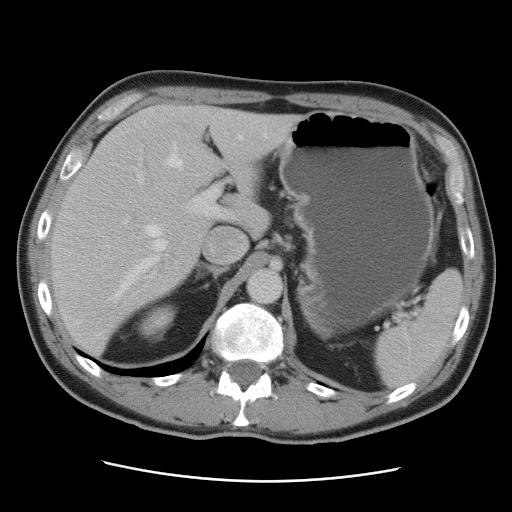
Contrast-enhanced abdominal CT, one axial slice. Slice 59 of 89 in the series (ordered by position). 120 kVp. Intravenous contrast given. Soft-tissue window (W 400 / L 40 HU). 5 mm slice thickness. 512 × 512 image matrix. Male patient, age 59 years. From the clinical record (not read from this slice): diagnosis: colorectal cancer liver metastases, imaged before liver resection; multiple liver metastases: yes; largest metastasis: 0.6 cm; disease in both lobes: yes.
Structures marked on this image (manually delineated by an expert):
- hepatic veins: bounding box <110,133,267,304> (left, top, right, bottom; pixels)
- liver: <50,105,300,355>
- planned liver remnant (the part of the liver to remain after resection): <81,105,270,239>
- portal vein (with intrahepatic branches): <125,168,223,224>